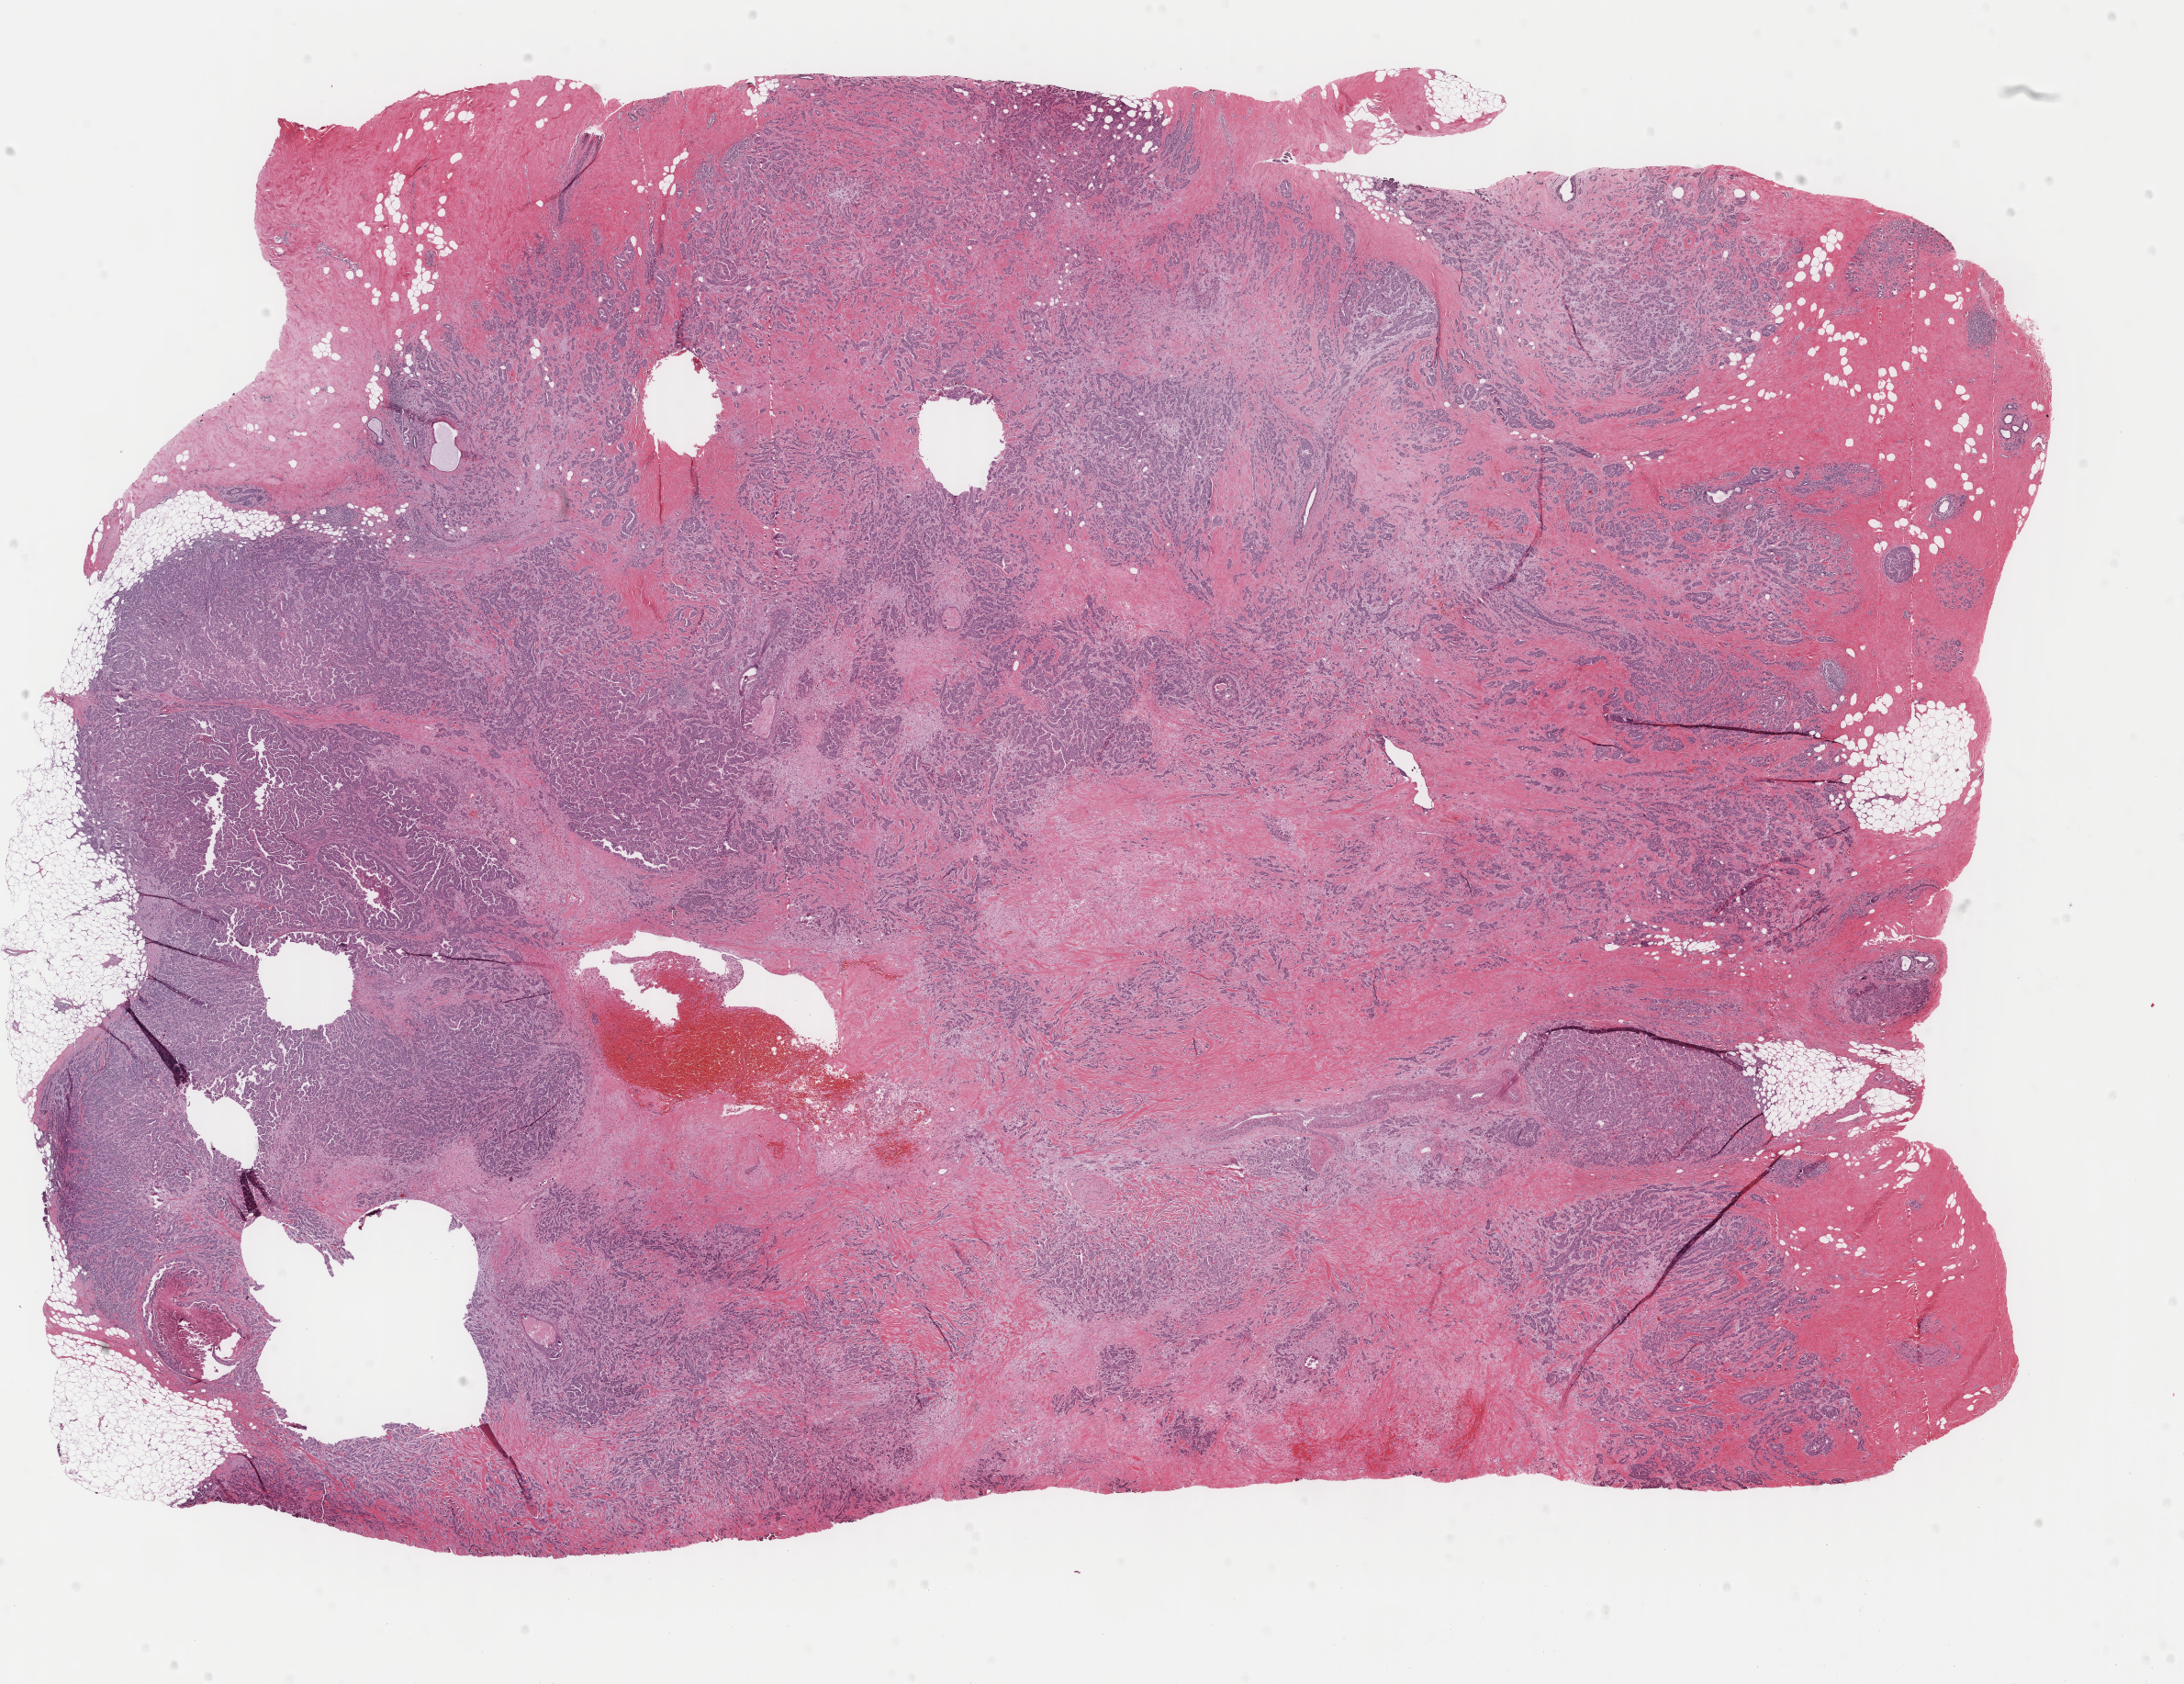
H&E whole-slide image, low-resolution overview of the scanned area, about 18.9 x 14.6 mm (from a 40x scan). FFPE section. Breast, primary tumour sample. Patient: female, age at initial diagnosis 52 years.
Histologic diagnosis: Infiltrating duct carcinoma, NOS. AJCC pathologic stage: IIB (6th edition). Lymph nodes positive (case pathology): 1 of 2 examined. Laterality: right.